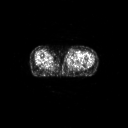
FDG PET of an extremity soft-tissue mass (from a PET/CT study), one axial slice. Position 51 of 91 along the scan axis. 128 × 128 image matrix, field of view 700 × 700 mm. Patient: female, 74 years. Case-level facts recorded for this patient, not image findings: histological type: pleomorphic leiomyosarcoma; grade: high; site of the primary tumour: left thigh.
Outlined on this slice (expert contour drawn on MRI and transferred to this co-registered scan by the dataset authors):
- gross tumour volume including surrounding oedema: box from (x=66, y=53) to (x=77, y=60) px